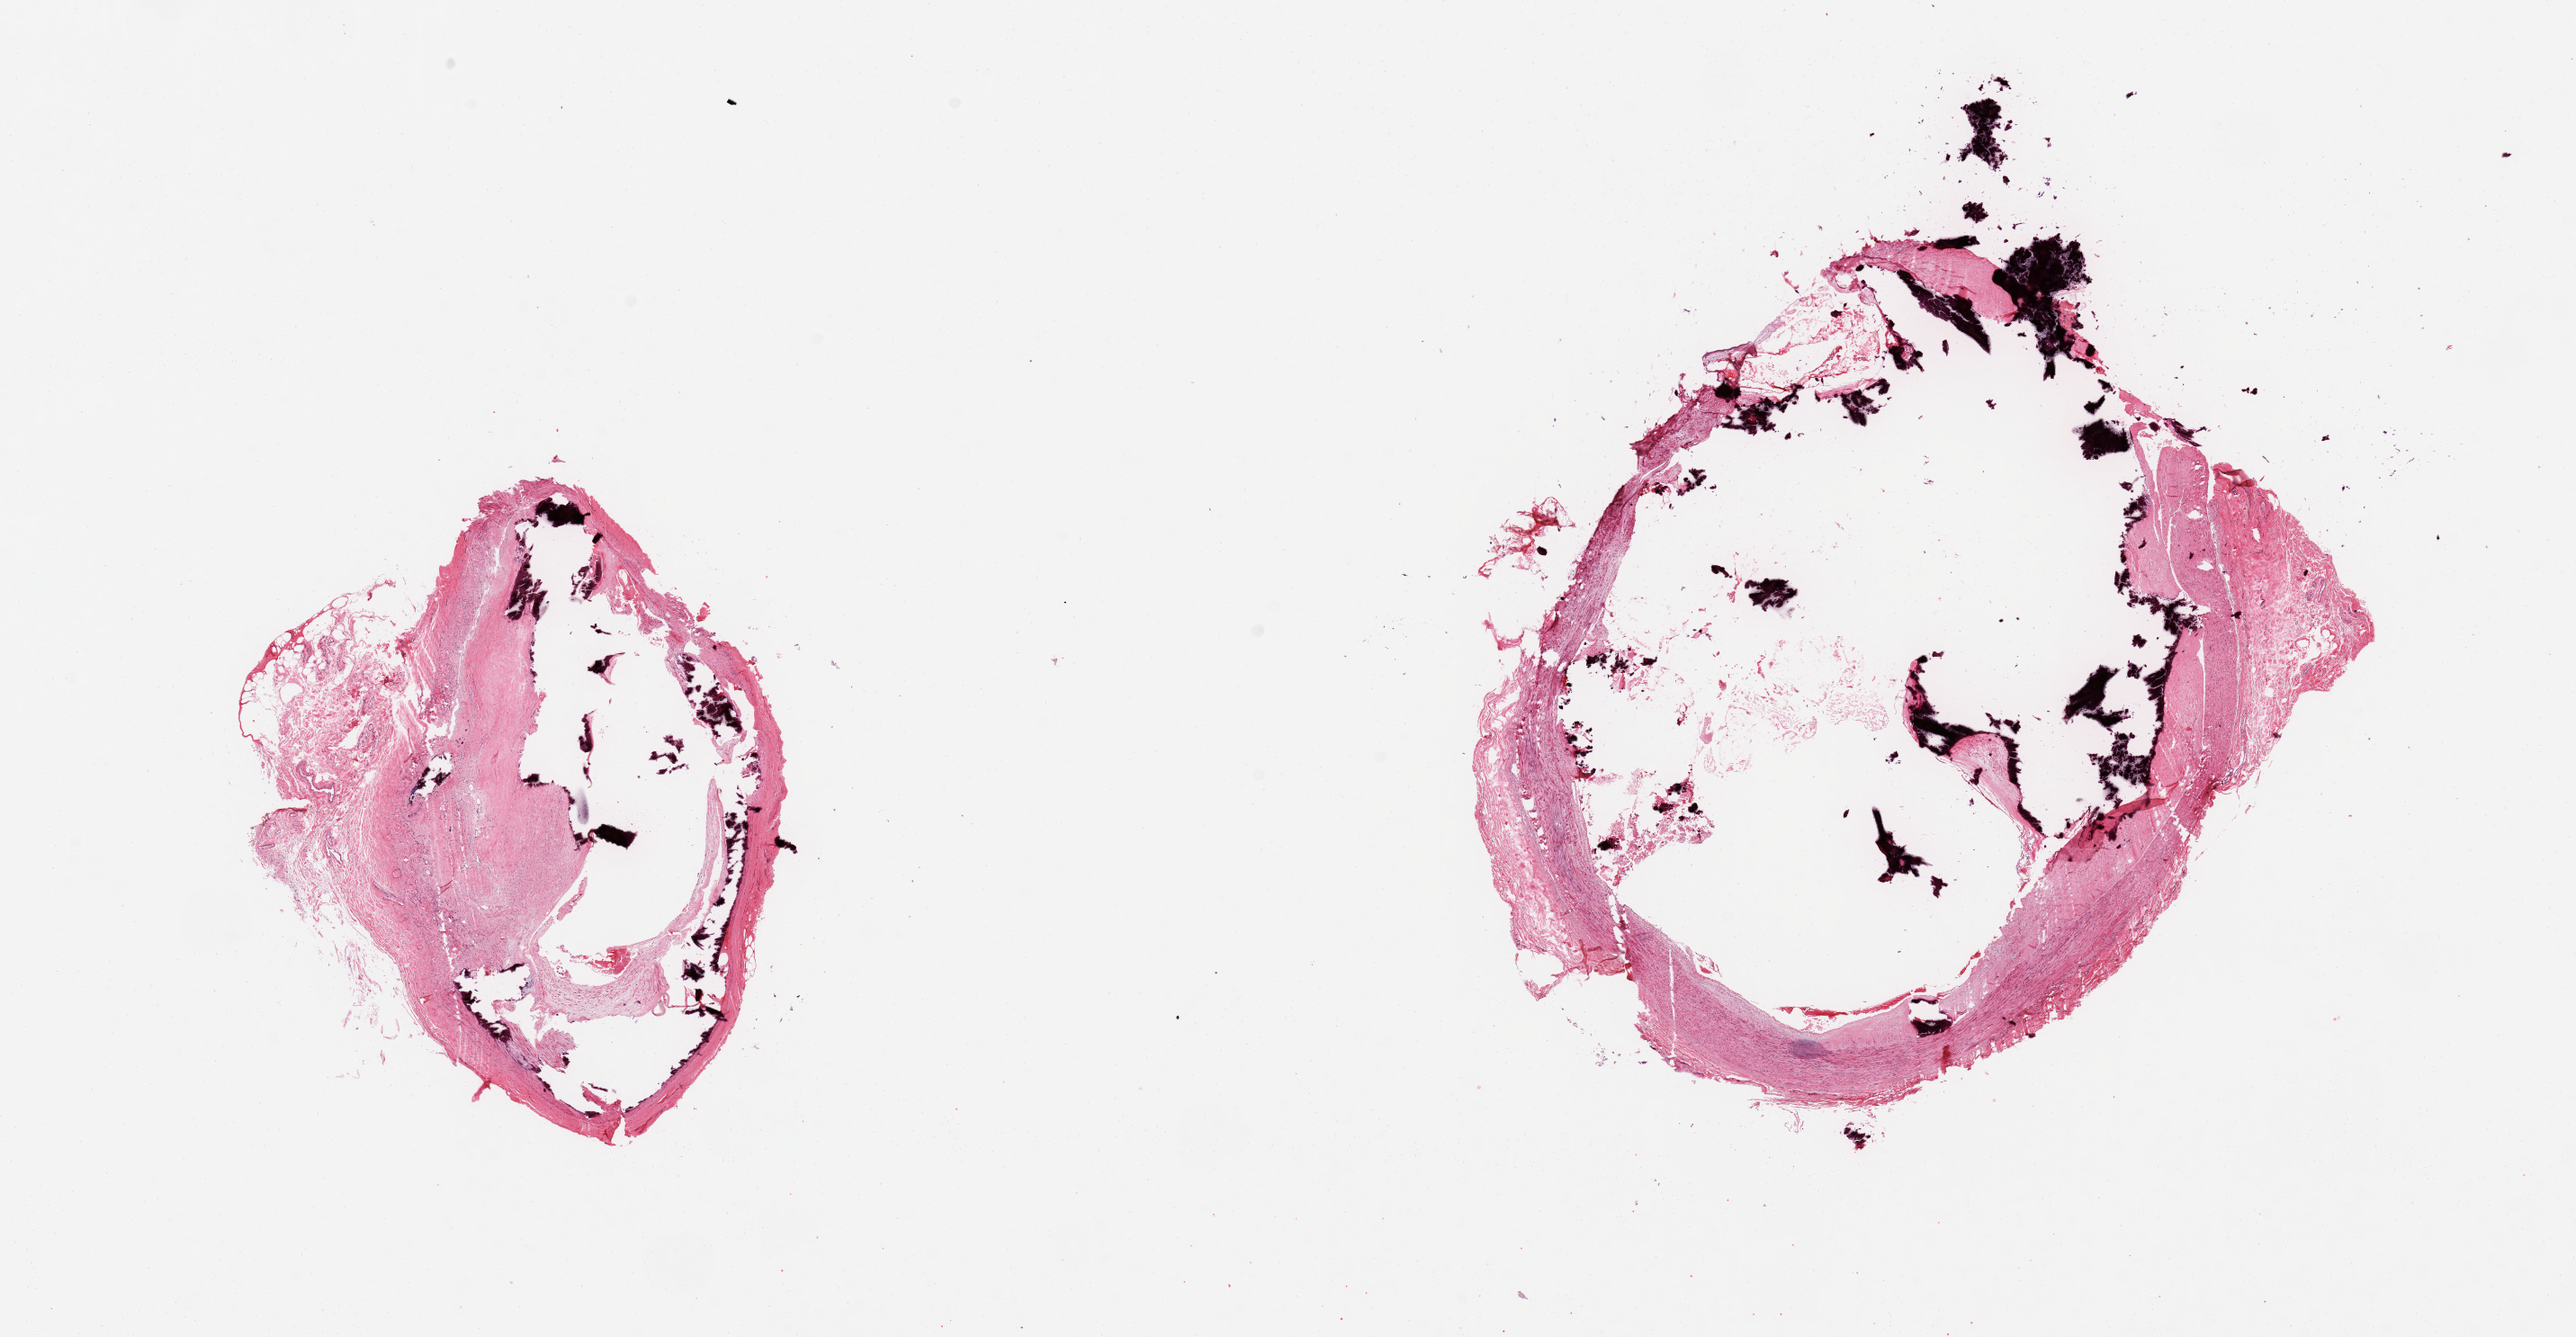
Haematoxylin and eosin whole-slide image — whole scanned area (about 22.6 x 11.8 mm, from a 20x scan) shown as a low-resolution overview. PAXgene-fixed paraffin-embedded (PFPE) section. Target tissue: tibial artery. Tissue donor sample.
Review note (as recorded): 2 pieces; extensive calcified atheromatous plaques centrally with thin rim of relatively normal wall at the periphery.